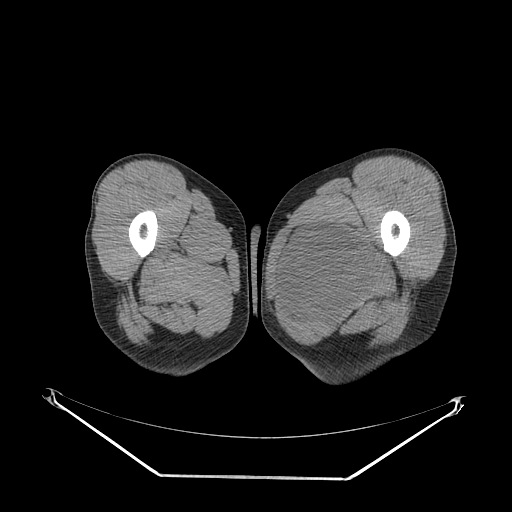
CT of an extremity soft-tissue mass (from a PET/CT study), one axial slice; position 29 of 267 along the scan axis; reconstruction kernel SOFT; soft-tissue window (W 400 / L 40 HU); 512 × 512 image matrix, field of view 500 × 500 mm. Male patient. From the clinical record (not read from this slice): histological type: pleiomorphic liposarcoma; grade: high; site of the primary tumour: left thigh.
Structures marked on this image (expert contour drawn on MRI and transferred to this co-registered scan by the dataset authors):
- gross tumour volume including surrounding oedema: bounding box (x1, y1, x2, y2) in pixels: (283, 221, 382, 320)
- gross tumour volume (mass): (286, 224, 378, 312)